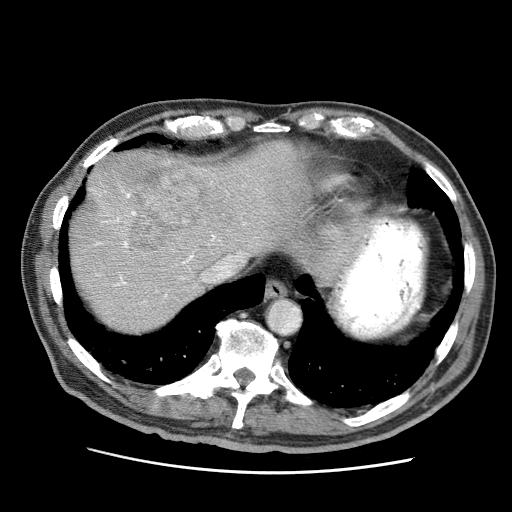
Contrast-enhanced abdominal CT (liver protocol), one axial slice; position 56 of 75 along the scan axis; reconstruction kernel STANDARD; 120 kVp; soft-tissue window (W 400 / L 40 HU); 512 × 512 image matrix, field of view 360 × 360 mm. From the clinical record (not read from this slice): diagnosis: hepatocellular carcinoma (patient treated with transarterial chemoembolisation; whether this scan precedes or follows treatment is not stated here); TNM stage (as recorded): Stage-IIIA; Child-Pugh class: A; tumour nodularity: multinodular; tumour size: 13.9 cm.
Structures marked on this image (semi-automatically segmented with operator editing):
- liver parenchyma outside the tumour (the mass and vessels are separate outlines, so this box may not span the whole liver): bounding box [x1, y1, x2, y2] px = [70, 140, 310, 330]
- mass: [84, 154, 208, 266]
- liver vessels: [96, 182, 246, 303]